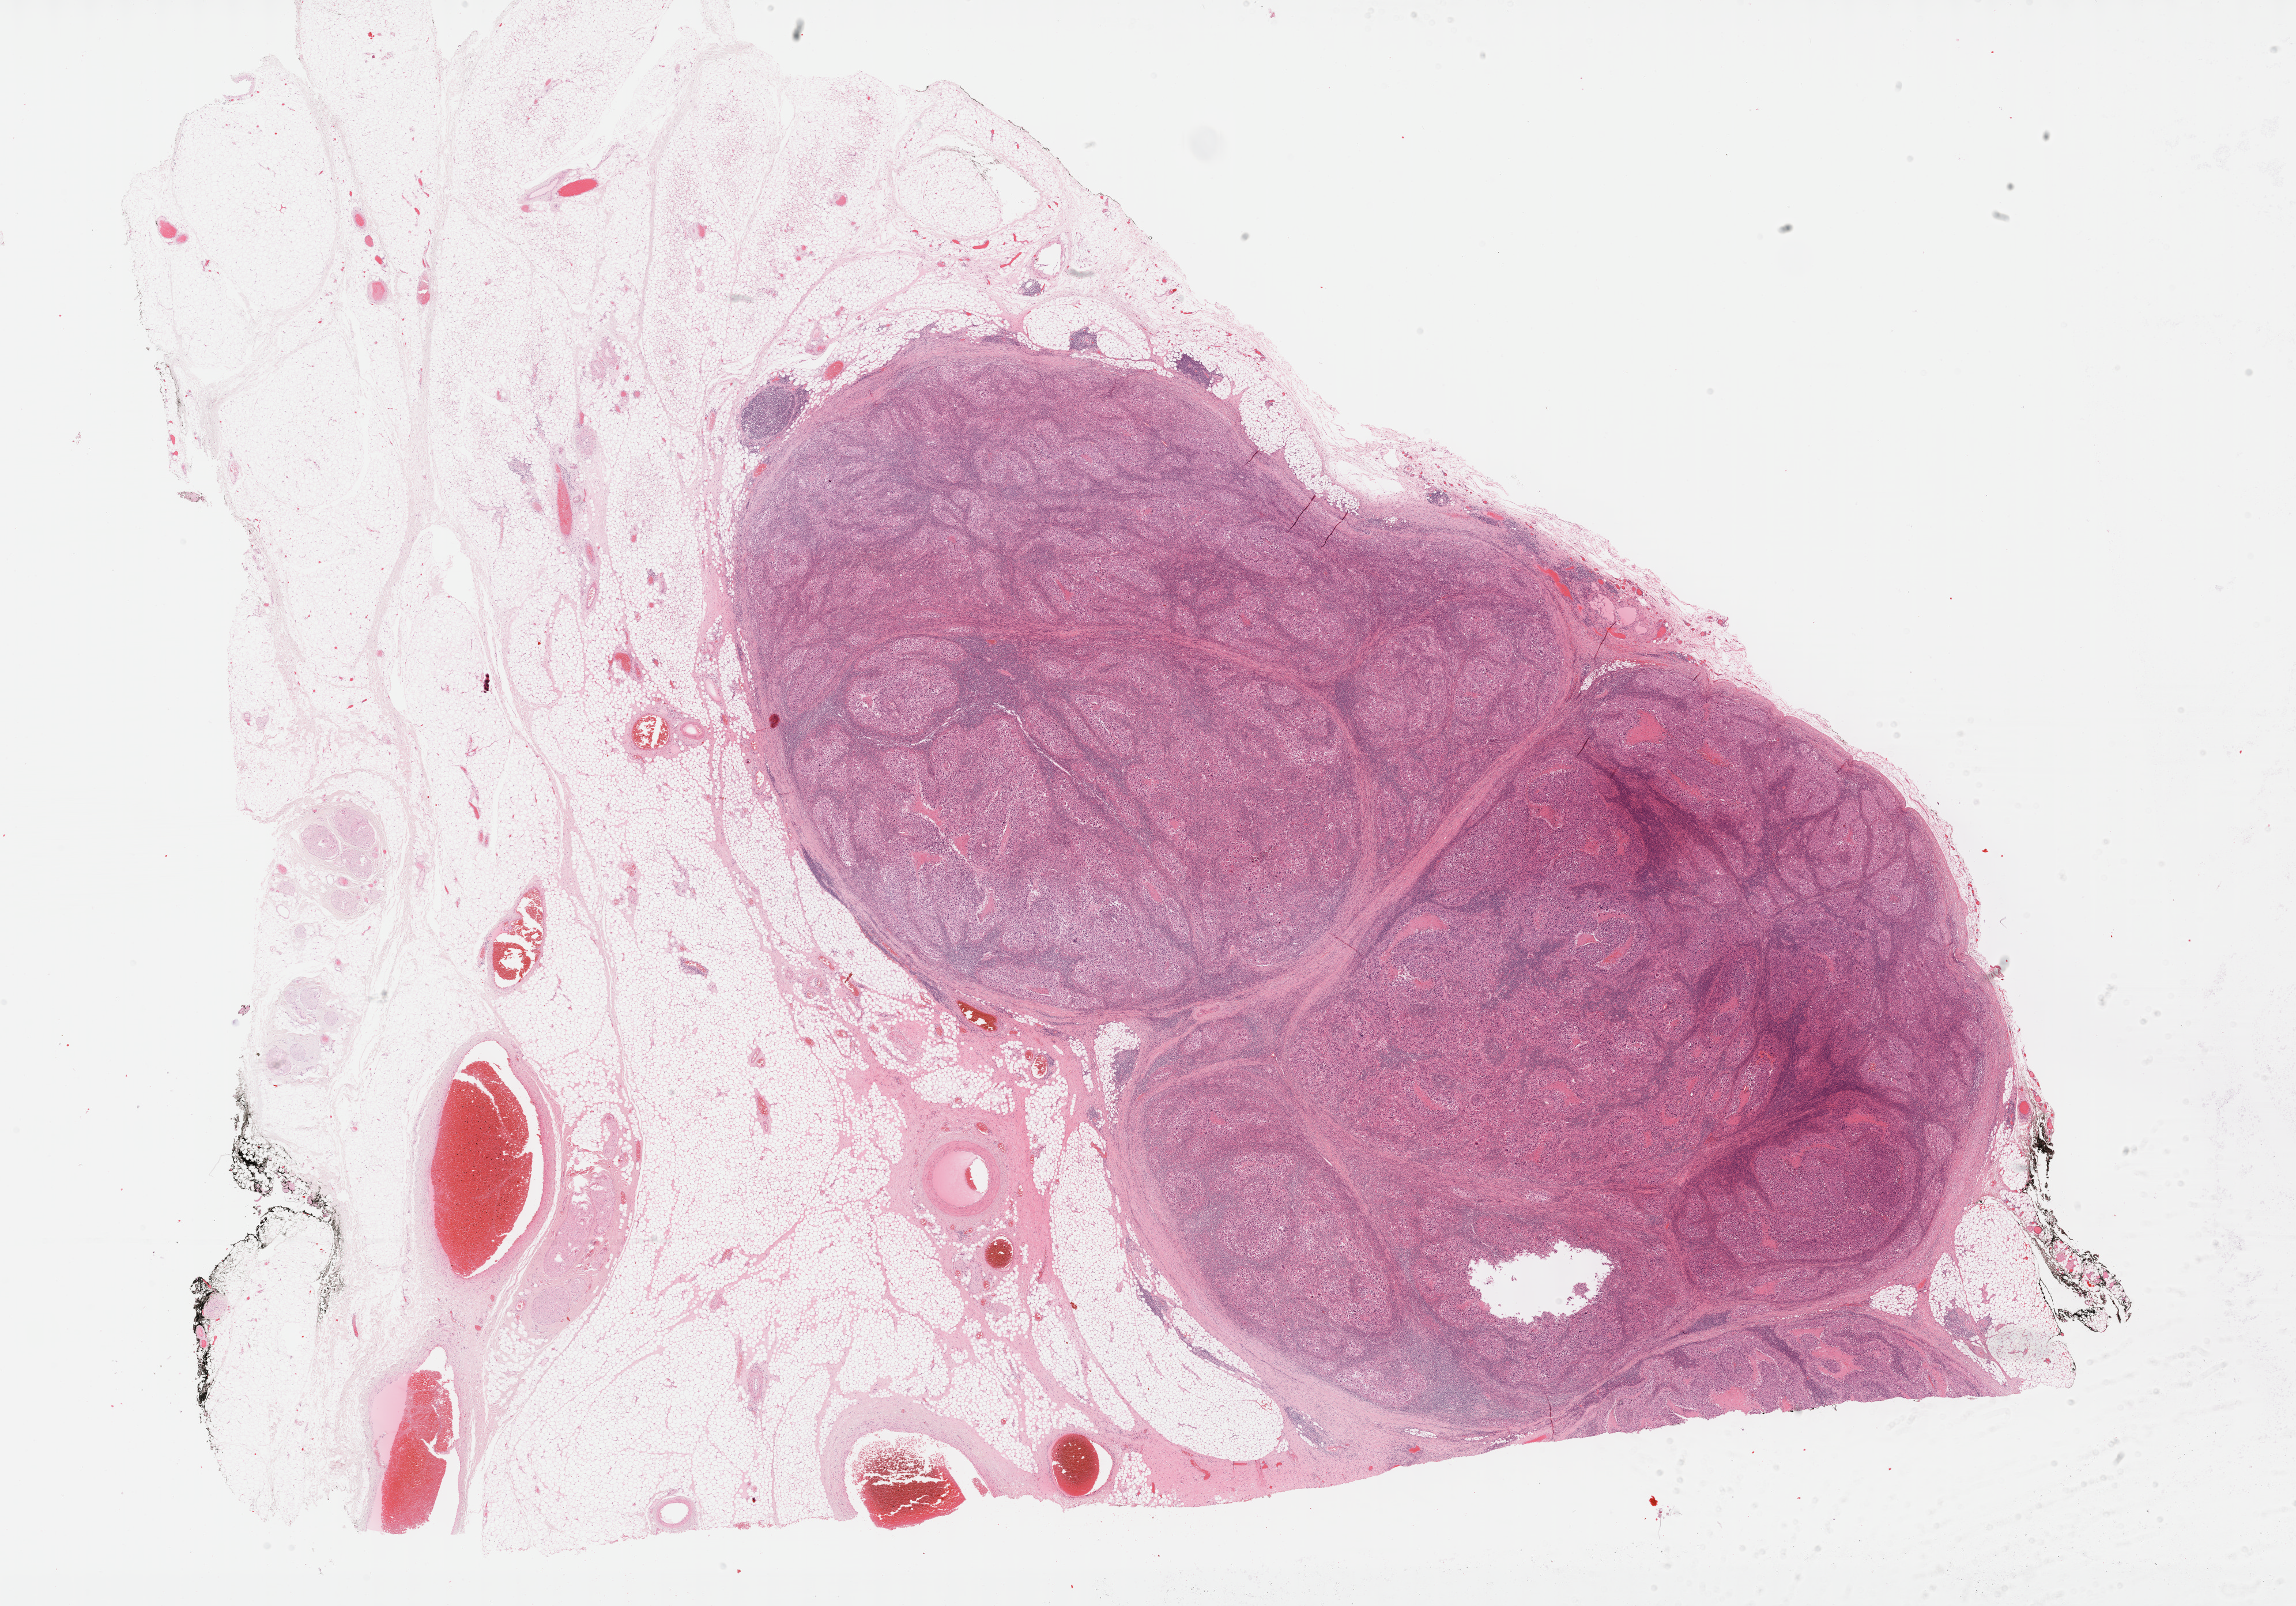
Whole-slide histology image, H&E — whole scanned area (about 32.2 x 22.5 mm, acquisition: 40x scan) shown as a low-resolution overview. Formalin-fixed paraffin-embedded (FFPE) diagnostic section. Metastatic tumour sample, sampled site: lymph nodes of axilla or arm. Male, age 45 years at initial diagnosis.
This section: metastatic tumour tissue. Patient diagnosis: Malignant melanoma, NOS.